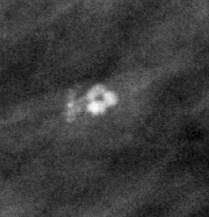
Crop from a digitized film mammogram around one marked abnormality; left breast; CC view.
Finding: calcifications, morphology round and regular / lucent center; BI-RADS assessment category 2; benign; no additional work-up was recommended (benign without callback).